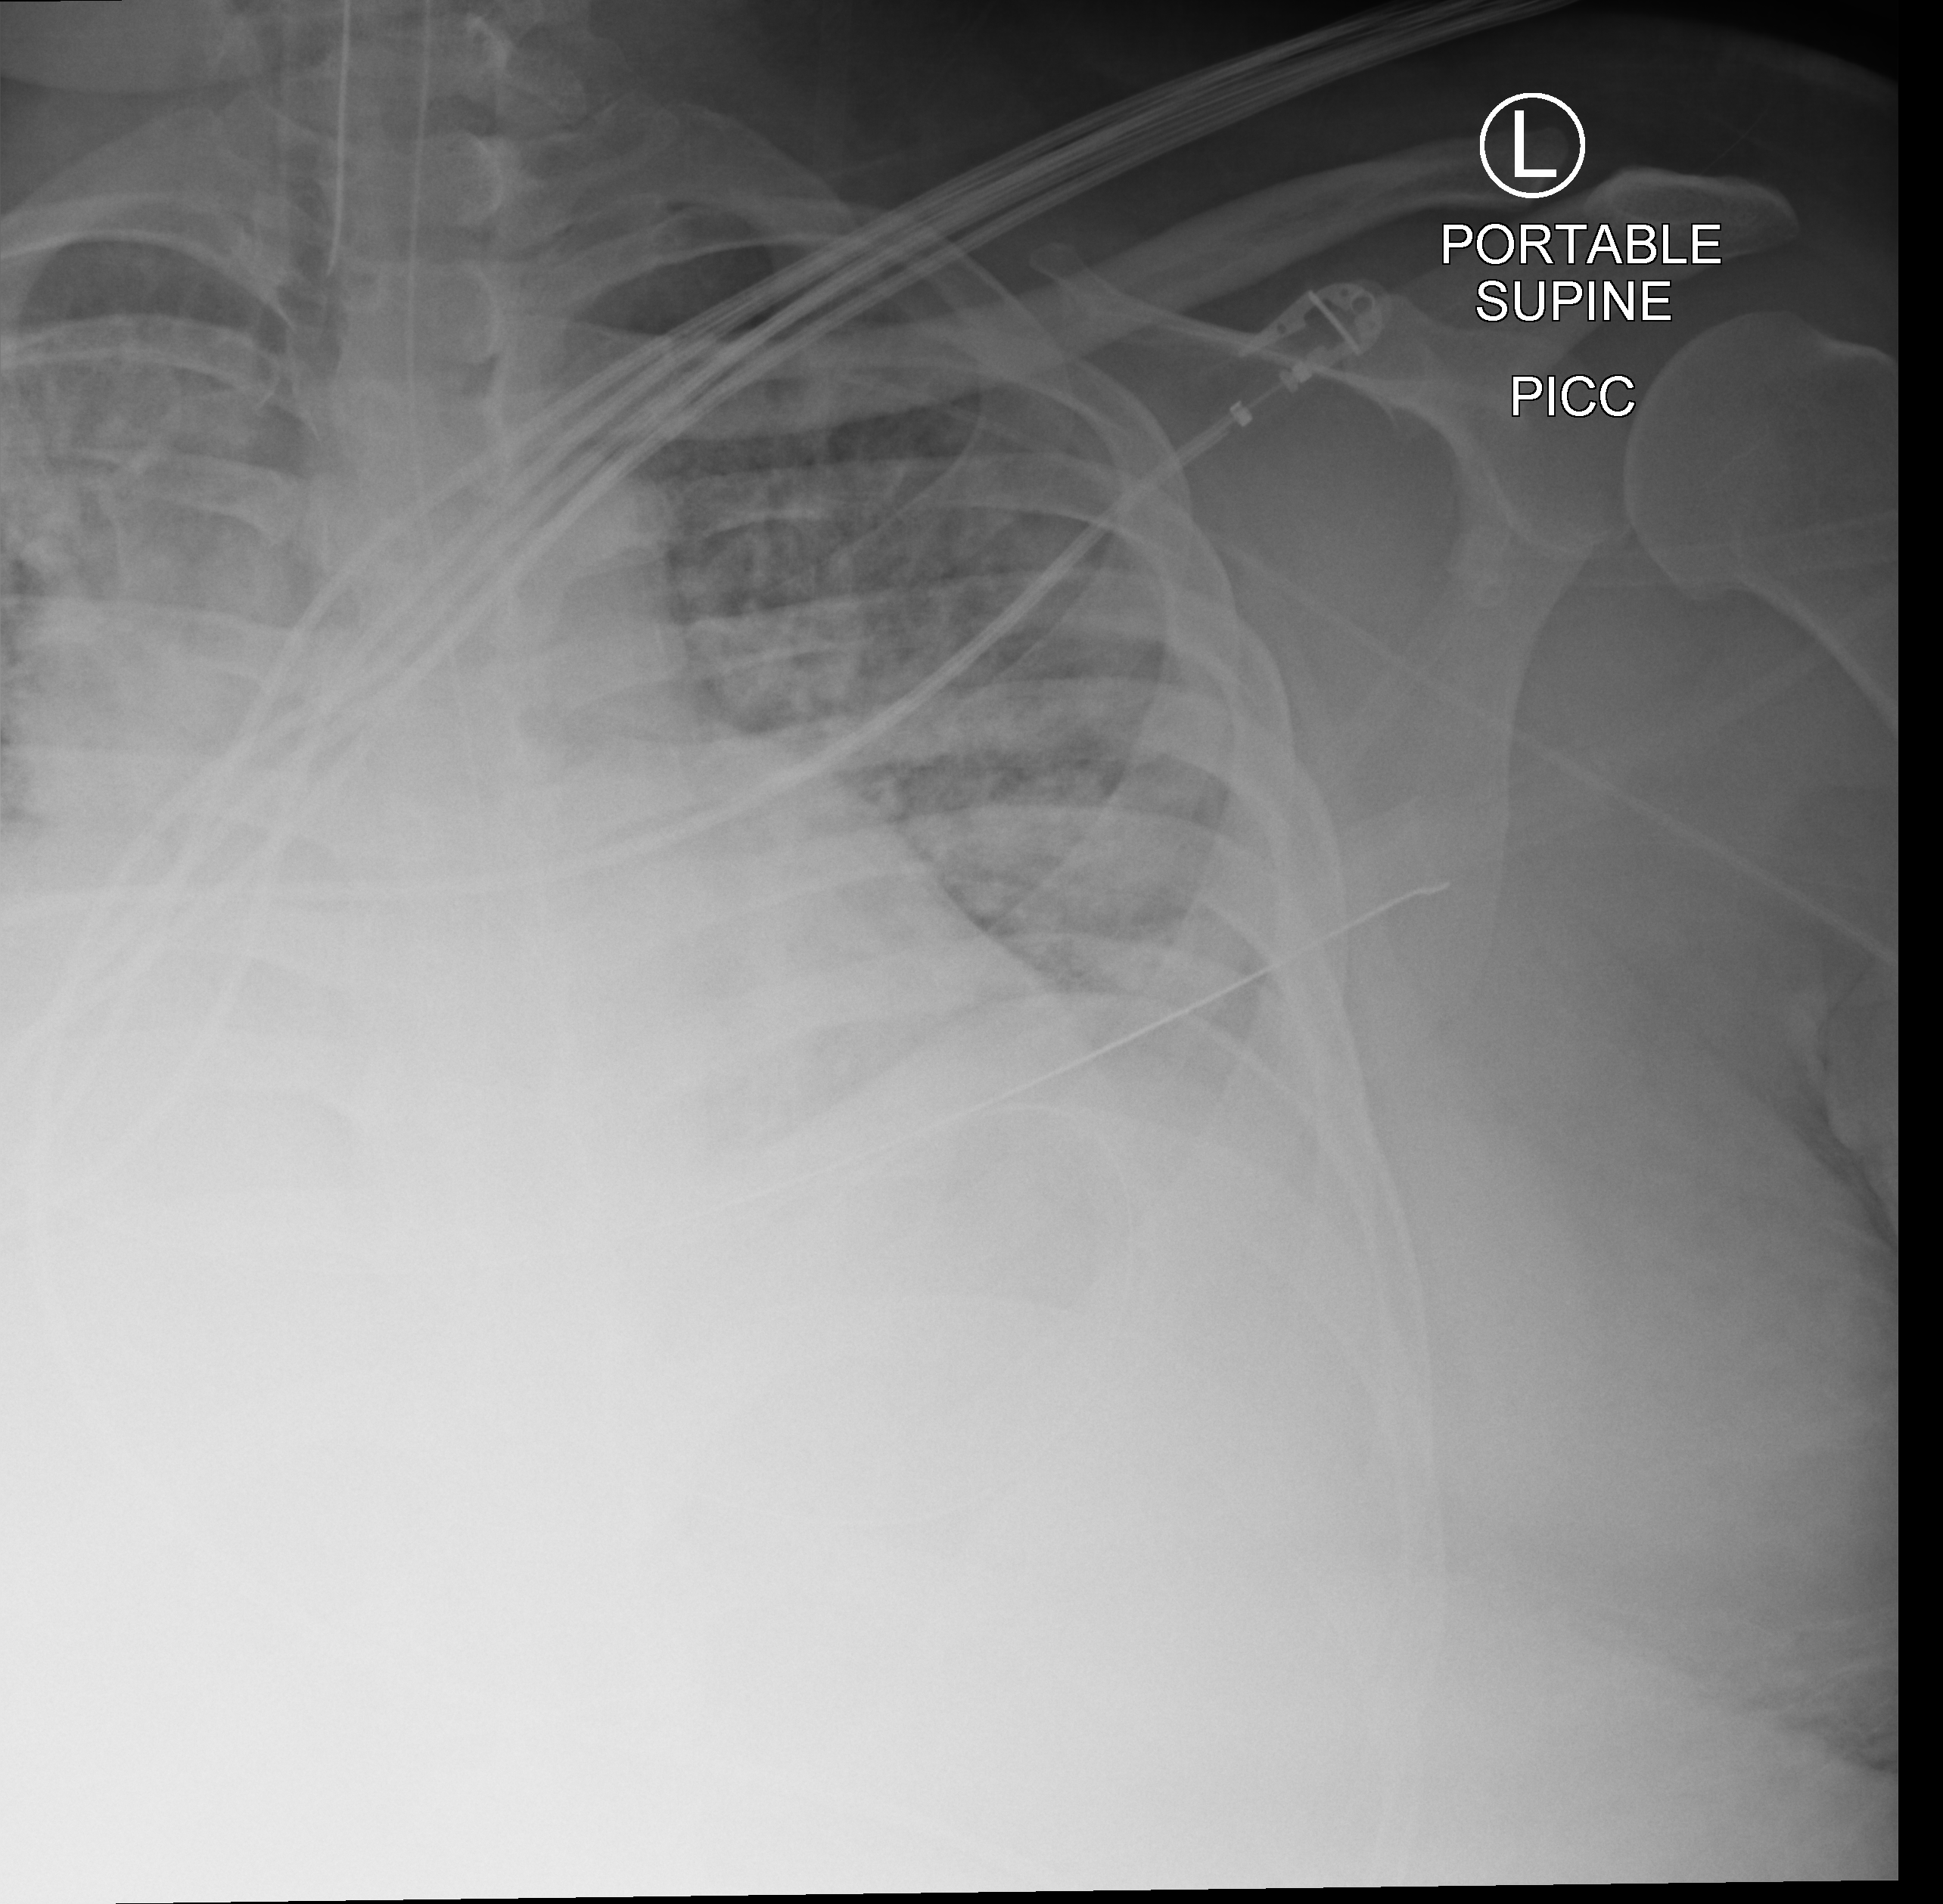
Chest X-ray (portable). Male patient hospitalised with COVID-19, age 18–59 years.
Hospital-stay facts (about this admission, not read from this image; timing relative to this image not recorded):
- smoking status (admission record): never
- COPD (admission record): yes
- admitted to intensive care during this hospital stay: yes